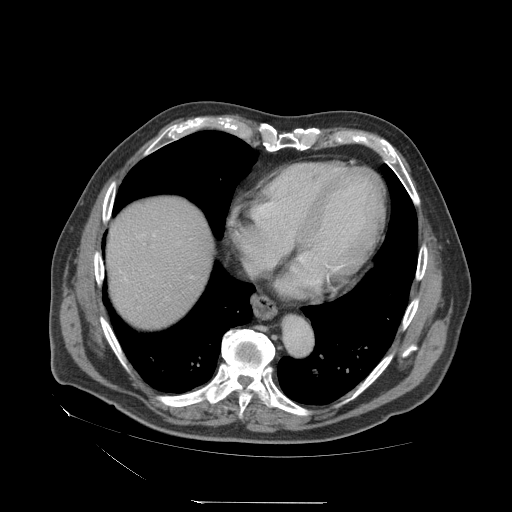
Contrast-enhanced abdominal CT (liver protocol), one axial slice. Position 68 of 83 along the scan axis. Reconstruction kernel STANDARD. Soft-tissue window (W 400 / L 40 HU). 2.5 mm slice thickness. 512 × 512 image matrix, field of view 460 × 460 mm. From the clinical record (not read from this slice): diagnosis: hepatocellular carcinoma (patient treated with transarterial chemoembolisation; whether this scan precedes or follows treatment is not stated here); TNM stage (as recorded): Stage-I; Child-Pugh class: A; tumour differentiation: well differentiated; tumour nodularity: uninodular.
Structures marked on this image (semi-automatically segmented with operator editing):
- liver parenchyma outside the tumour (the mass and vessels are separate outlines, so this box may not span the whole liver): box from (x=106, y=198) to (x=212, y=326) px